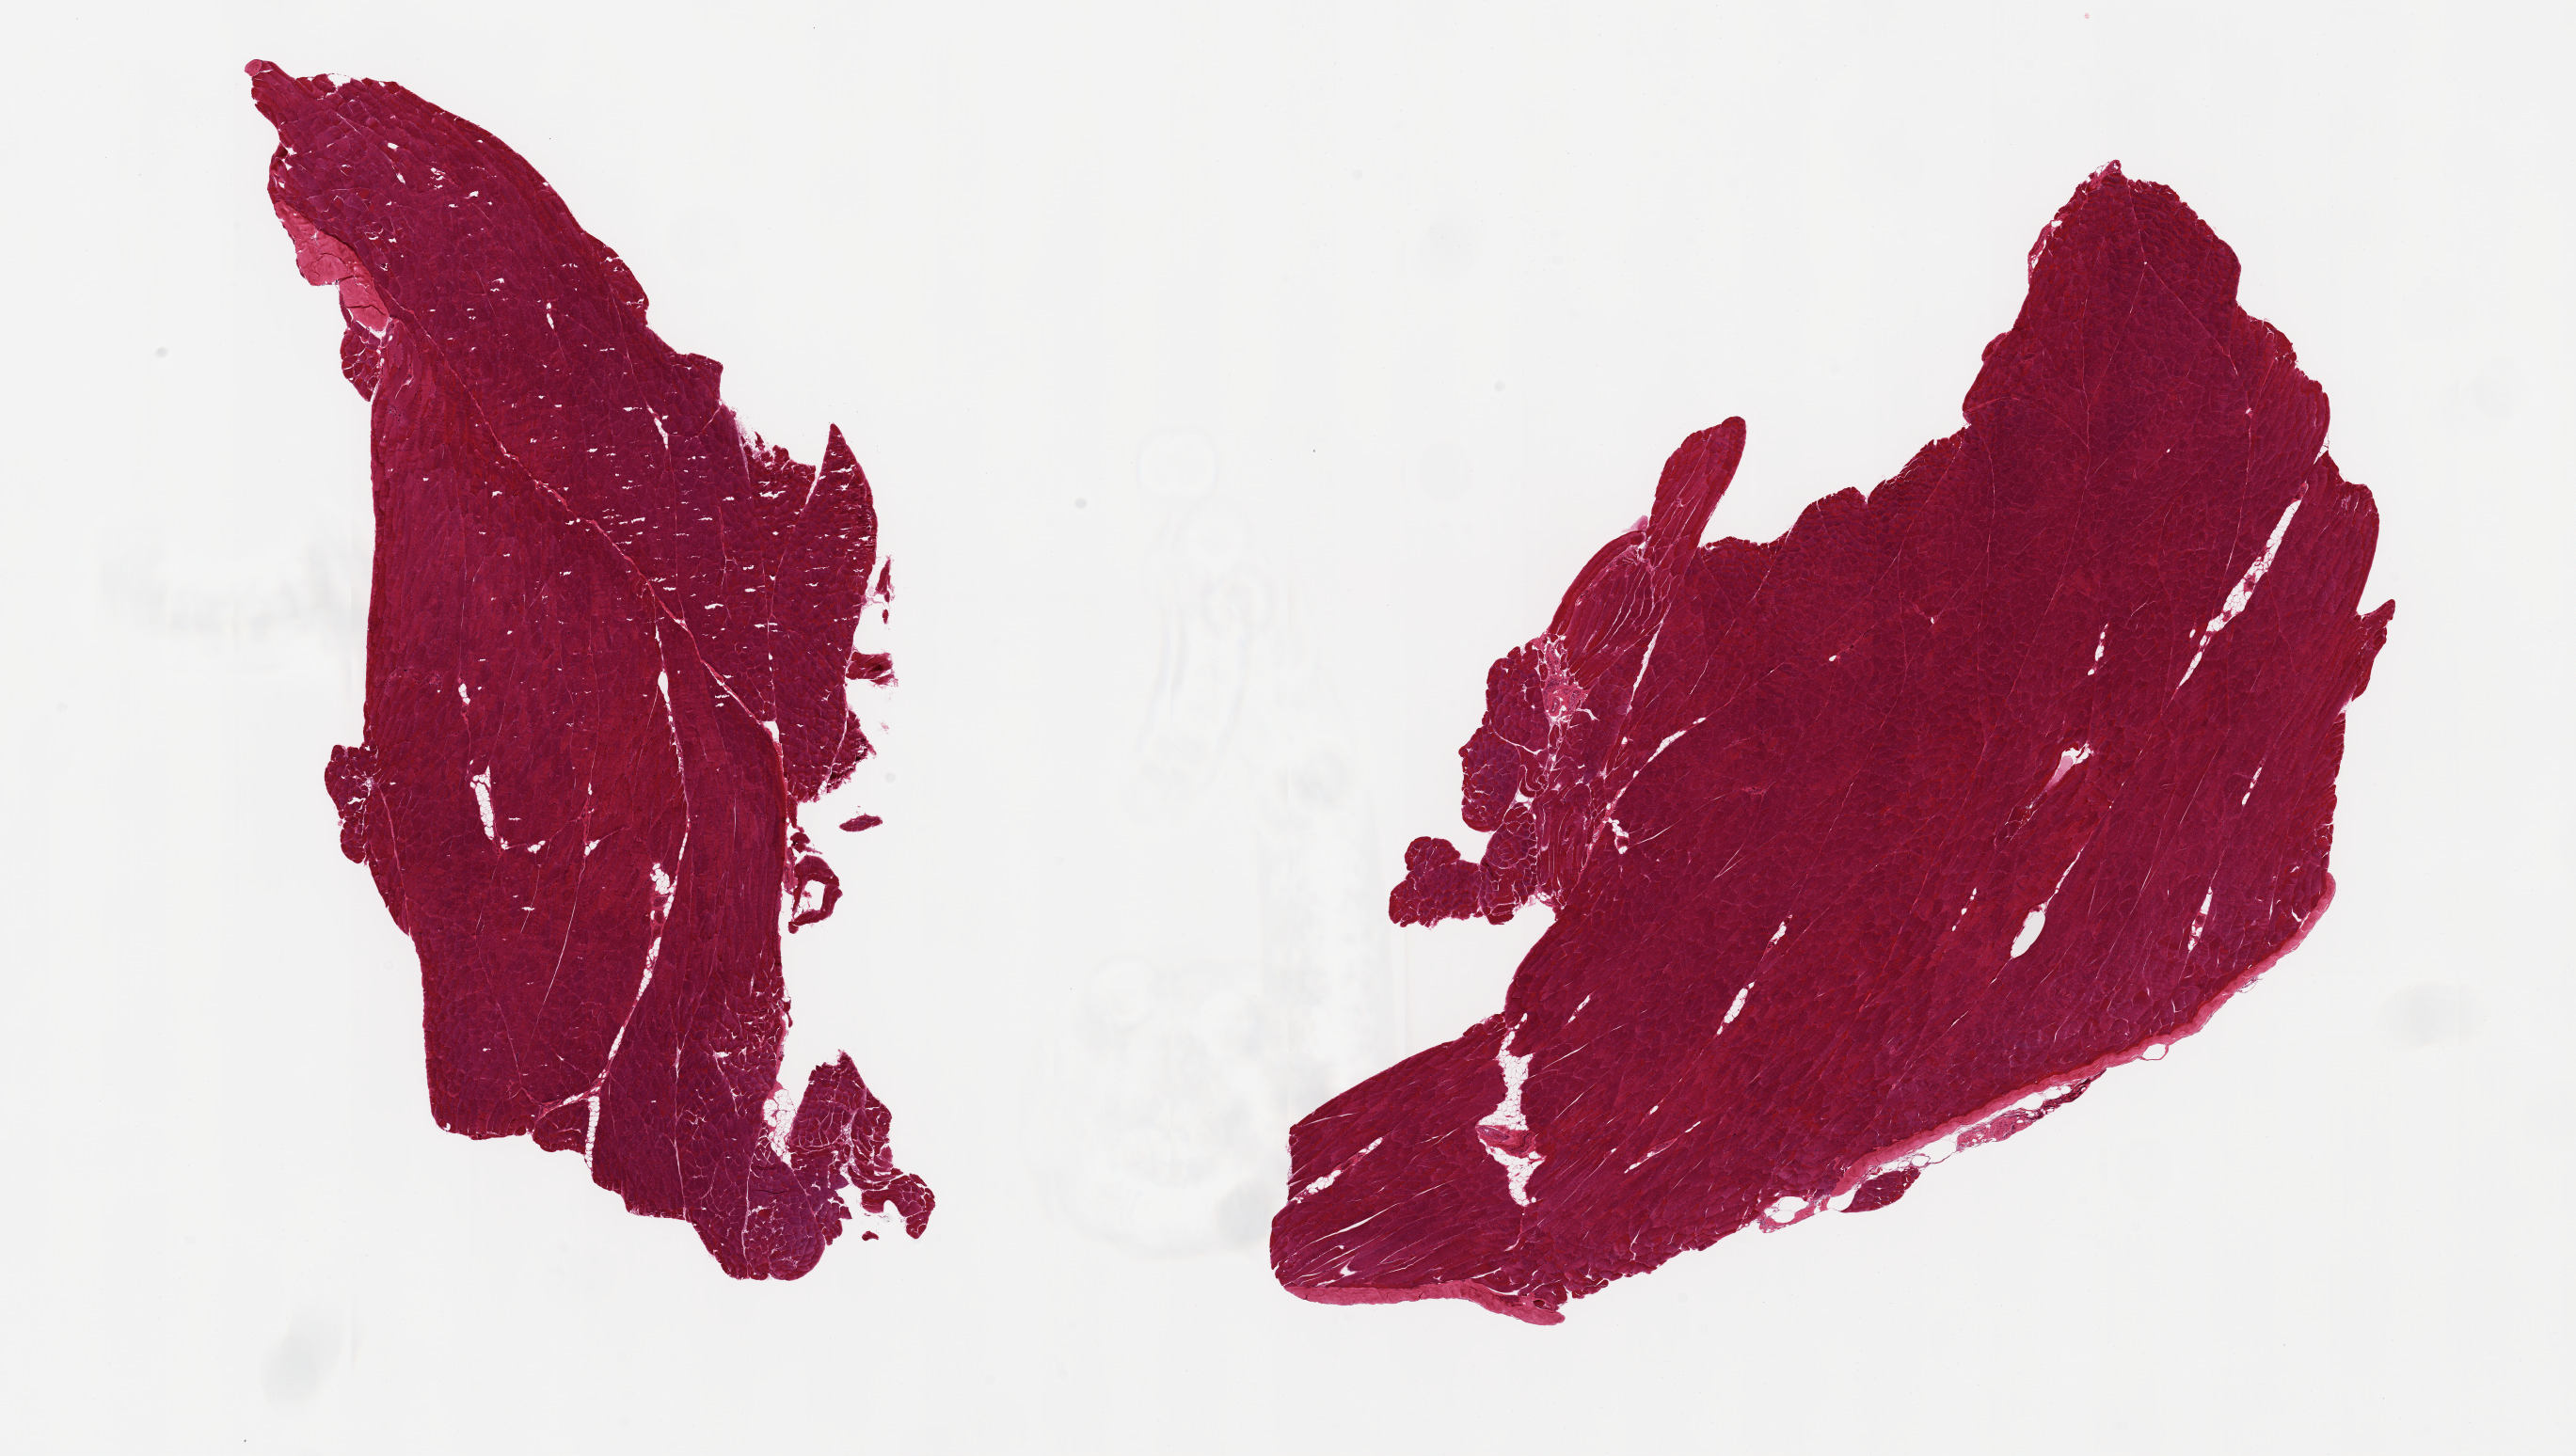
Hematoxylin and eosin (H&E) whole-slide image, brightfield — low-resolution overview of the scanned area, about 21.7 x 12.2 mm; PAXgene-fixed paraffin-embedded (PFPE) section; sampled site (target tissue): skeletal muscle; donor tissue sample. Male donor.
* reviewer comment on this tissue sample: 2 aliquots, ~10x5mm, essentially no interstitial fat